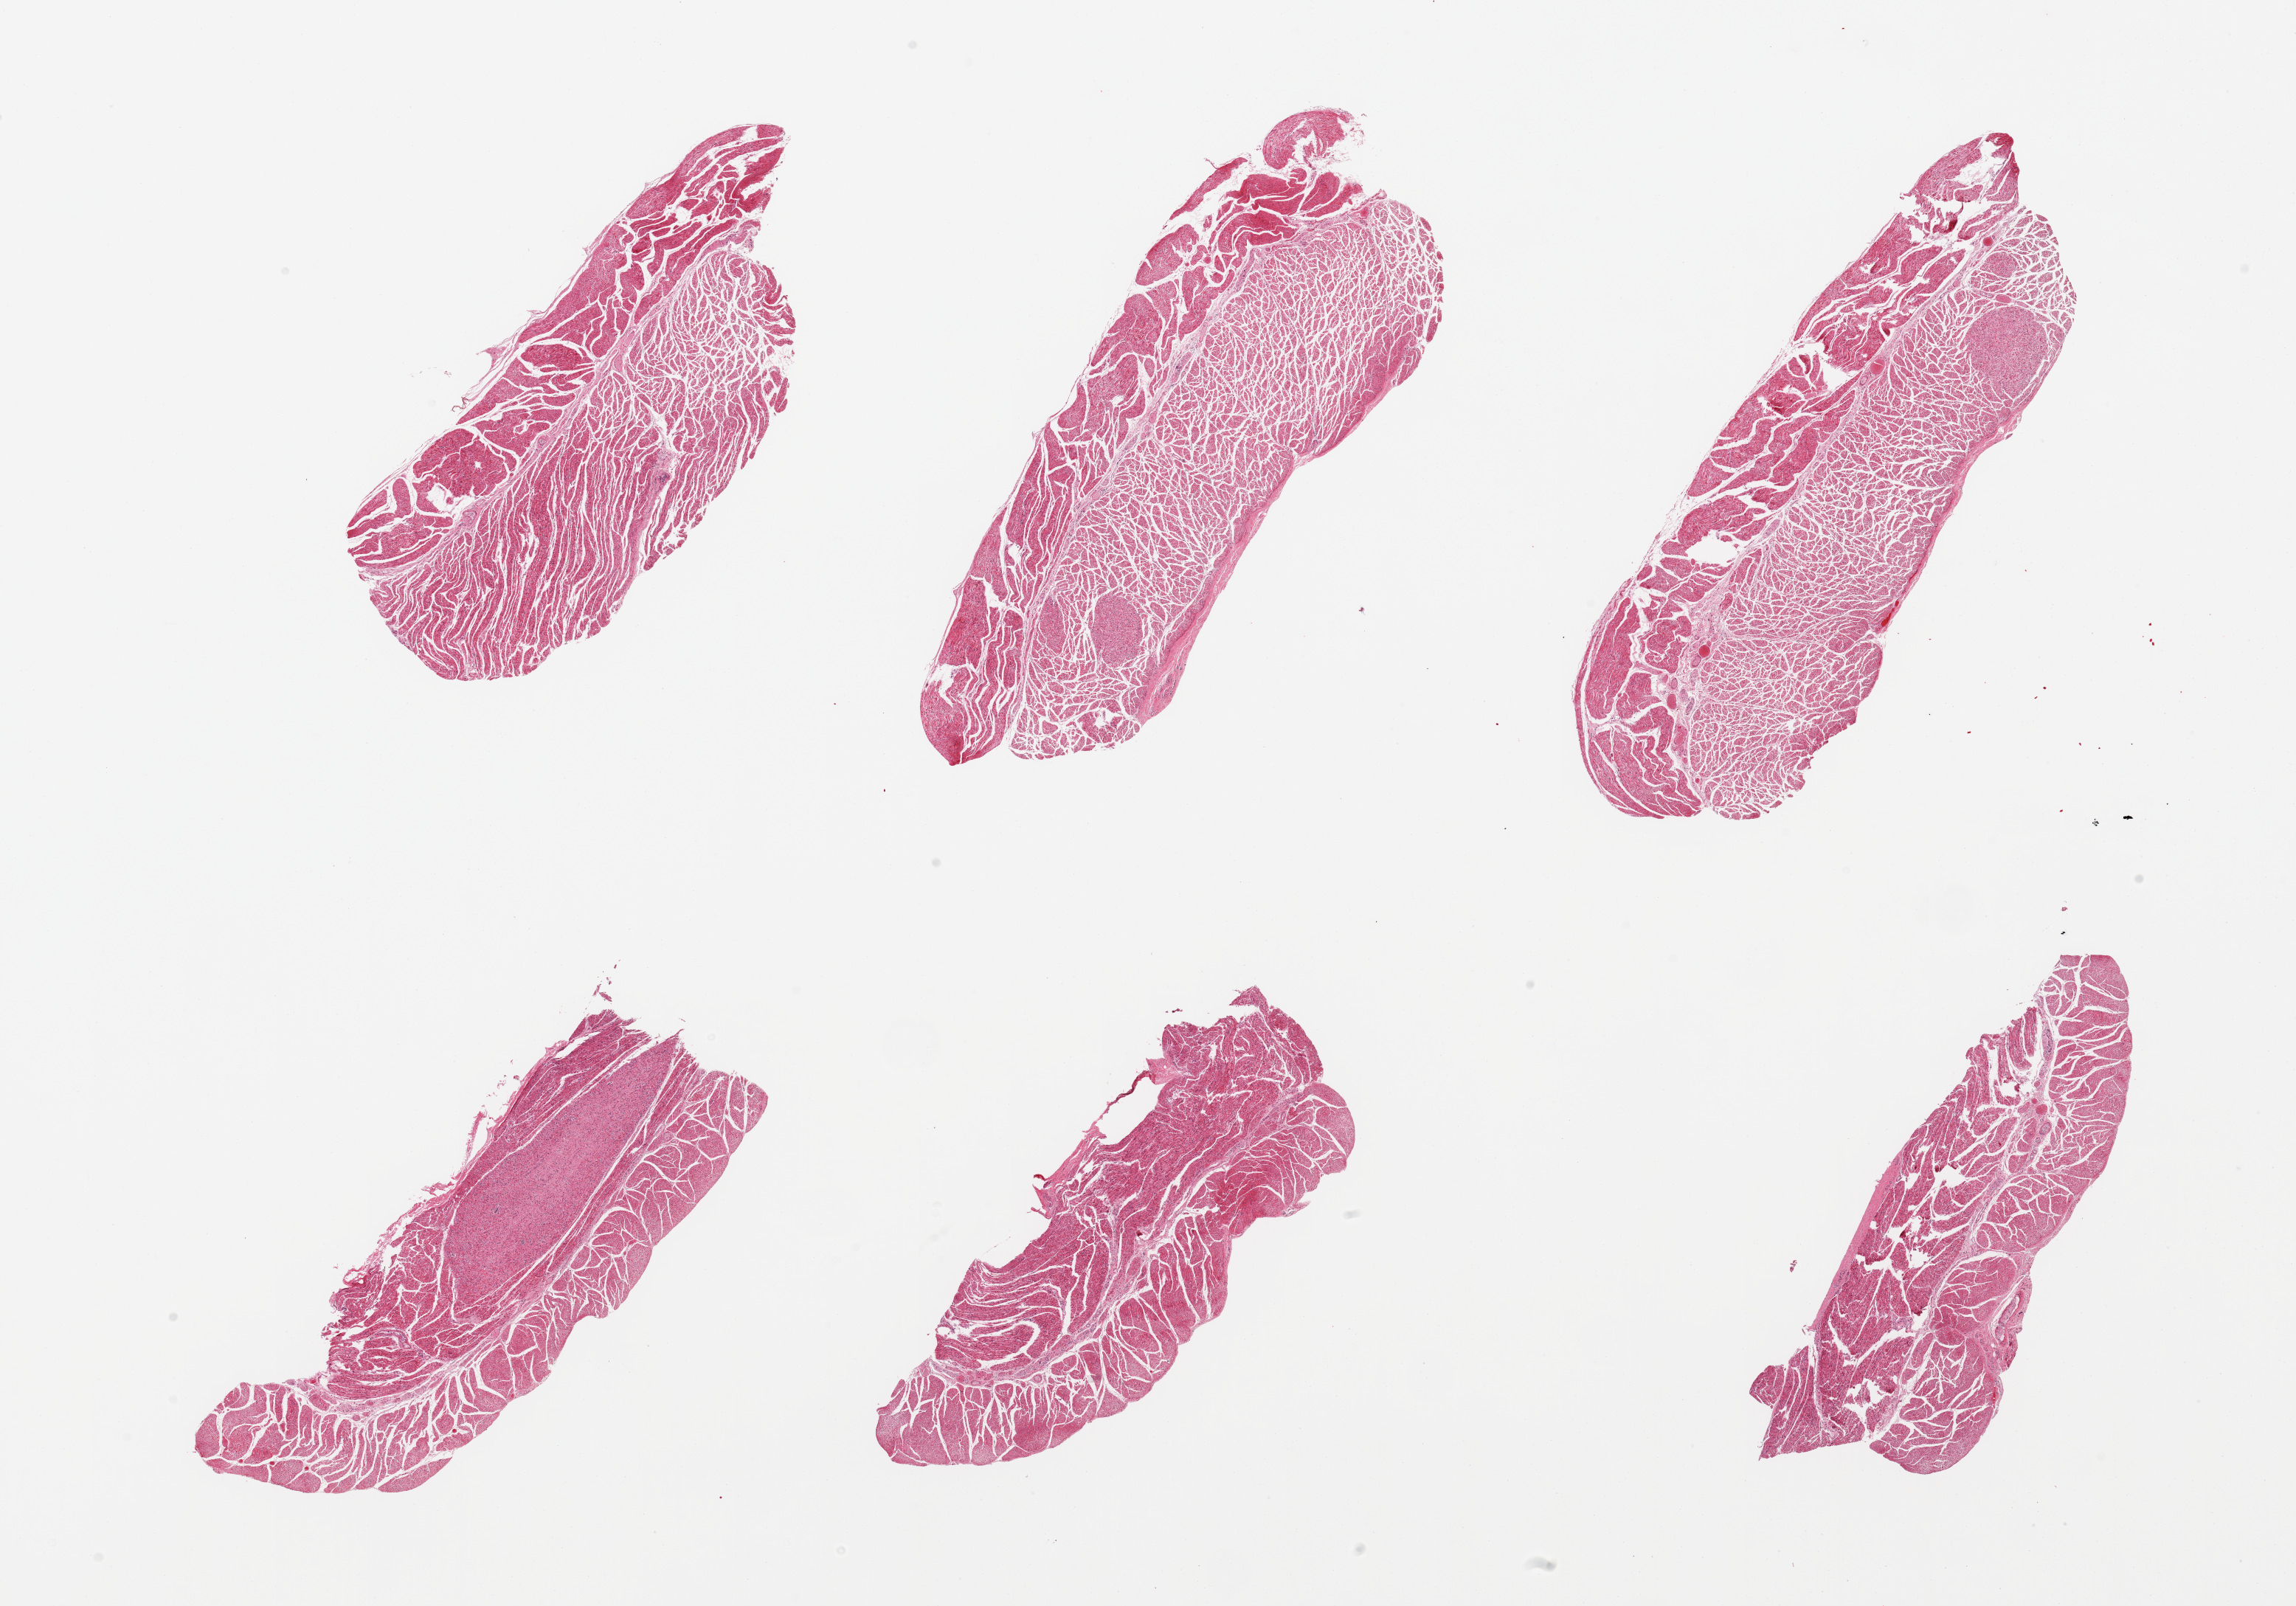
Digitized H&E-stained section, brightfield — low-resolution overview of the scanned area, about 24.6 x 17.2 mm; PAXgene-fixed, paraffin-embedded tissue; section of esophageal muscle (target tissue); tissue donor sample. Female donor.
• review note (as recorded): 6 pieces; target muscularis, well trimmed, unusual cylindrical muscle bundles